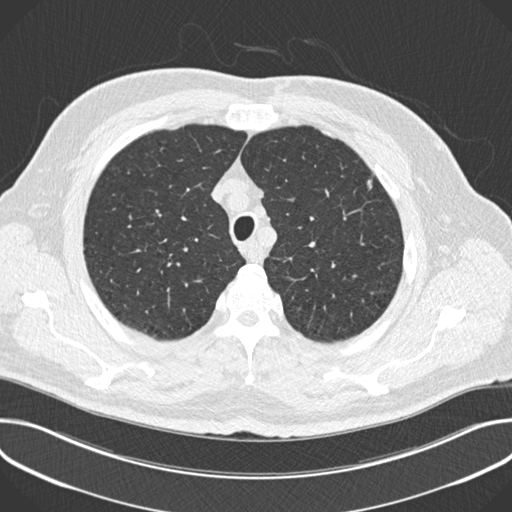
Low-dose screening chest CT, axial slice; baseline annual screen; lung window (W 1500 / L -600 HU); 2 mm slice thickness; slice 52 of 245 in the series; 512 × 512 image matrix, field of view 380 × 380 mm. Male participant, aged 63 years at enrolment. Current smoker at enrolment.
• Lesion marked by an expert reader, bounding box [x1, y1, x2, y2] px = [356, 169, 384, 201].
• The screening reader recorded 2 non-calcified nodules or masses ≥4 mm on this exam (left upper lobe, left upper lobe); which of them this box marks is not recorded.
• Participant outcome: lung cancer diagnosed 174 days after this screen — adenocarcinoma, NOS, left upper lobe, poorly differentiated (G3), stage IIIA (AJCC 6th edition), 11 mm at pathology.